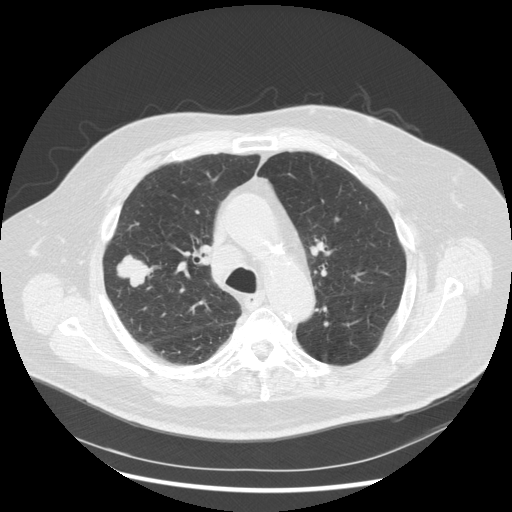
Low-dose screening chest CT, one axial slice; slice 192 of 263 in the series (ordered by position); reconstruction kernel STANDARD; 120 kVp; lung window (W 1500 / L -600 HU); 2.5 mm slice thickness; 512 × 512 image matrix, field of view 400 × 400 mm.
Structures marked on this image (expert manual segmentation):
- lesion 1 (tumor, upper lobe of right lung): box from (x=117, y=255) to (x=153, y=289) px